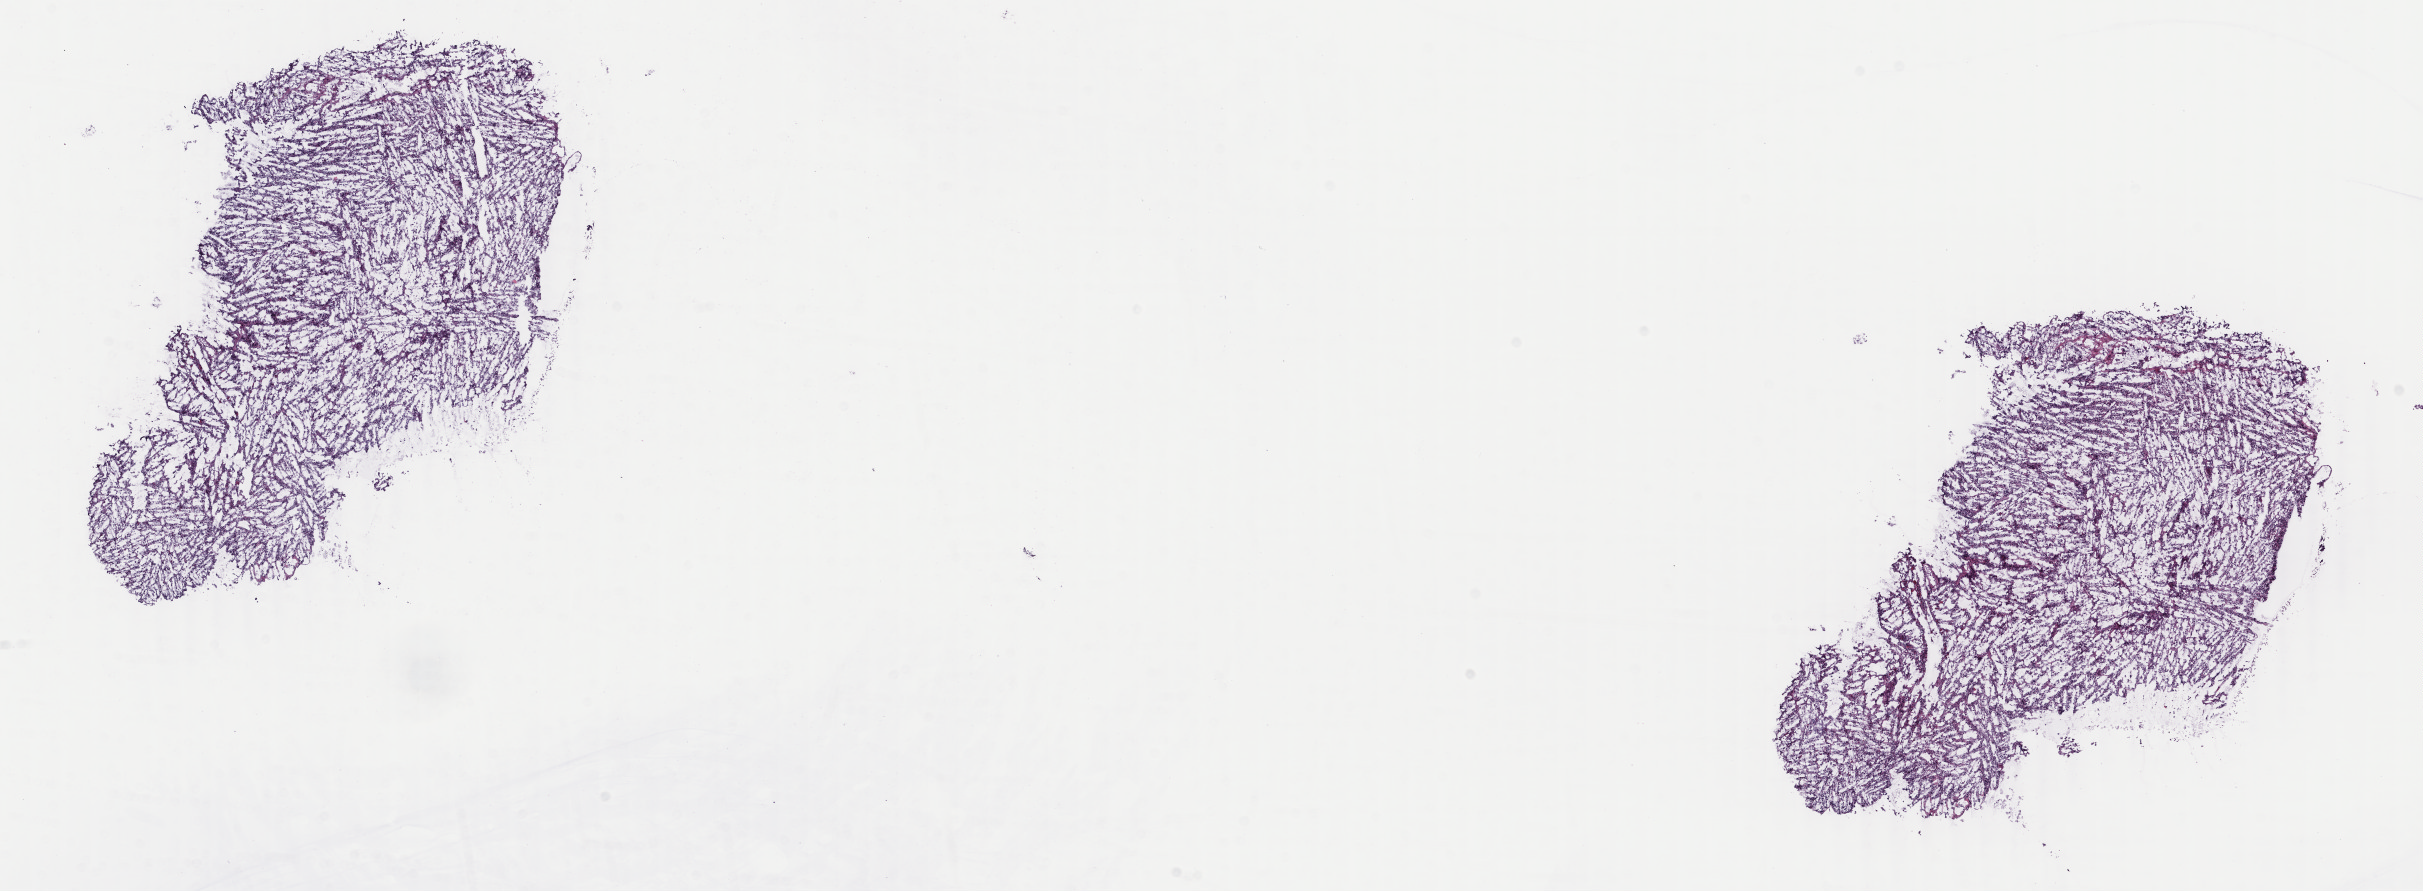
Whole-slide histology image, H&E-stained, shown as a low-resolution overview of the whole scanned area (about 19.3 x 7.1 mm, slide scanned at 40x); frozen section from the top of the tissue portion; primary tumour sample from the uterus. Female patient; age at initial diagnosis 70 years. Composition of this section per pathologist review: tumour cells 80%, tumour nuclei 80%, normal cells 5%, stromal cells 5%, necrosis 10%. Infiltration values recorded for this section: lymphocyte infiltration 70%, monocyte infiltration 15%, neutrophil infiltration 5%.
FIGO stage: II. Lymph nodes positive (case pathology): 0 of 4 examined. Pathologic diagnosis: Mullerian mixed tumor.